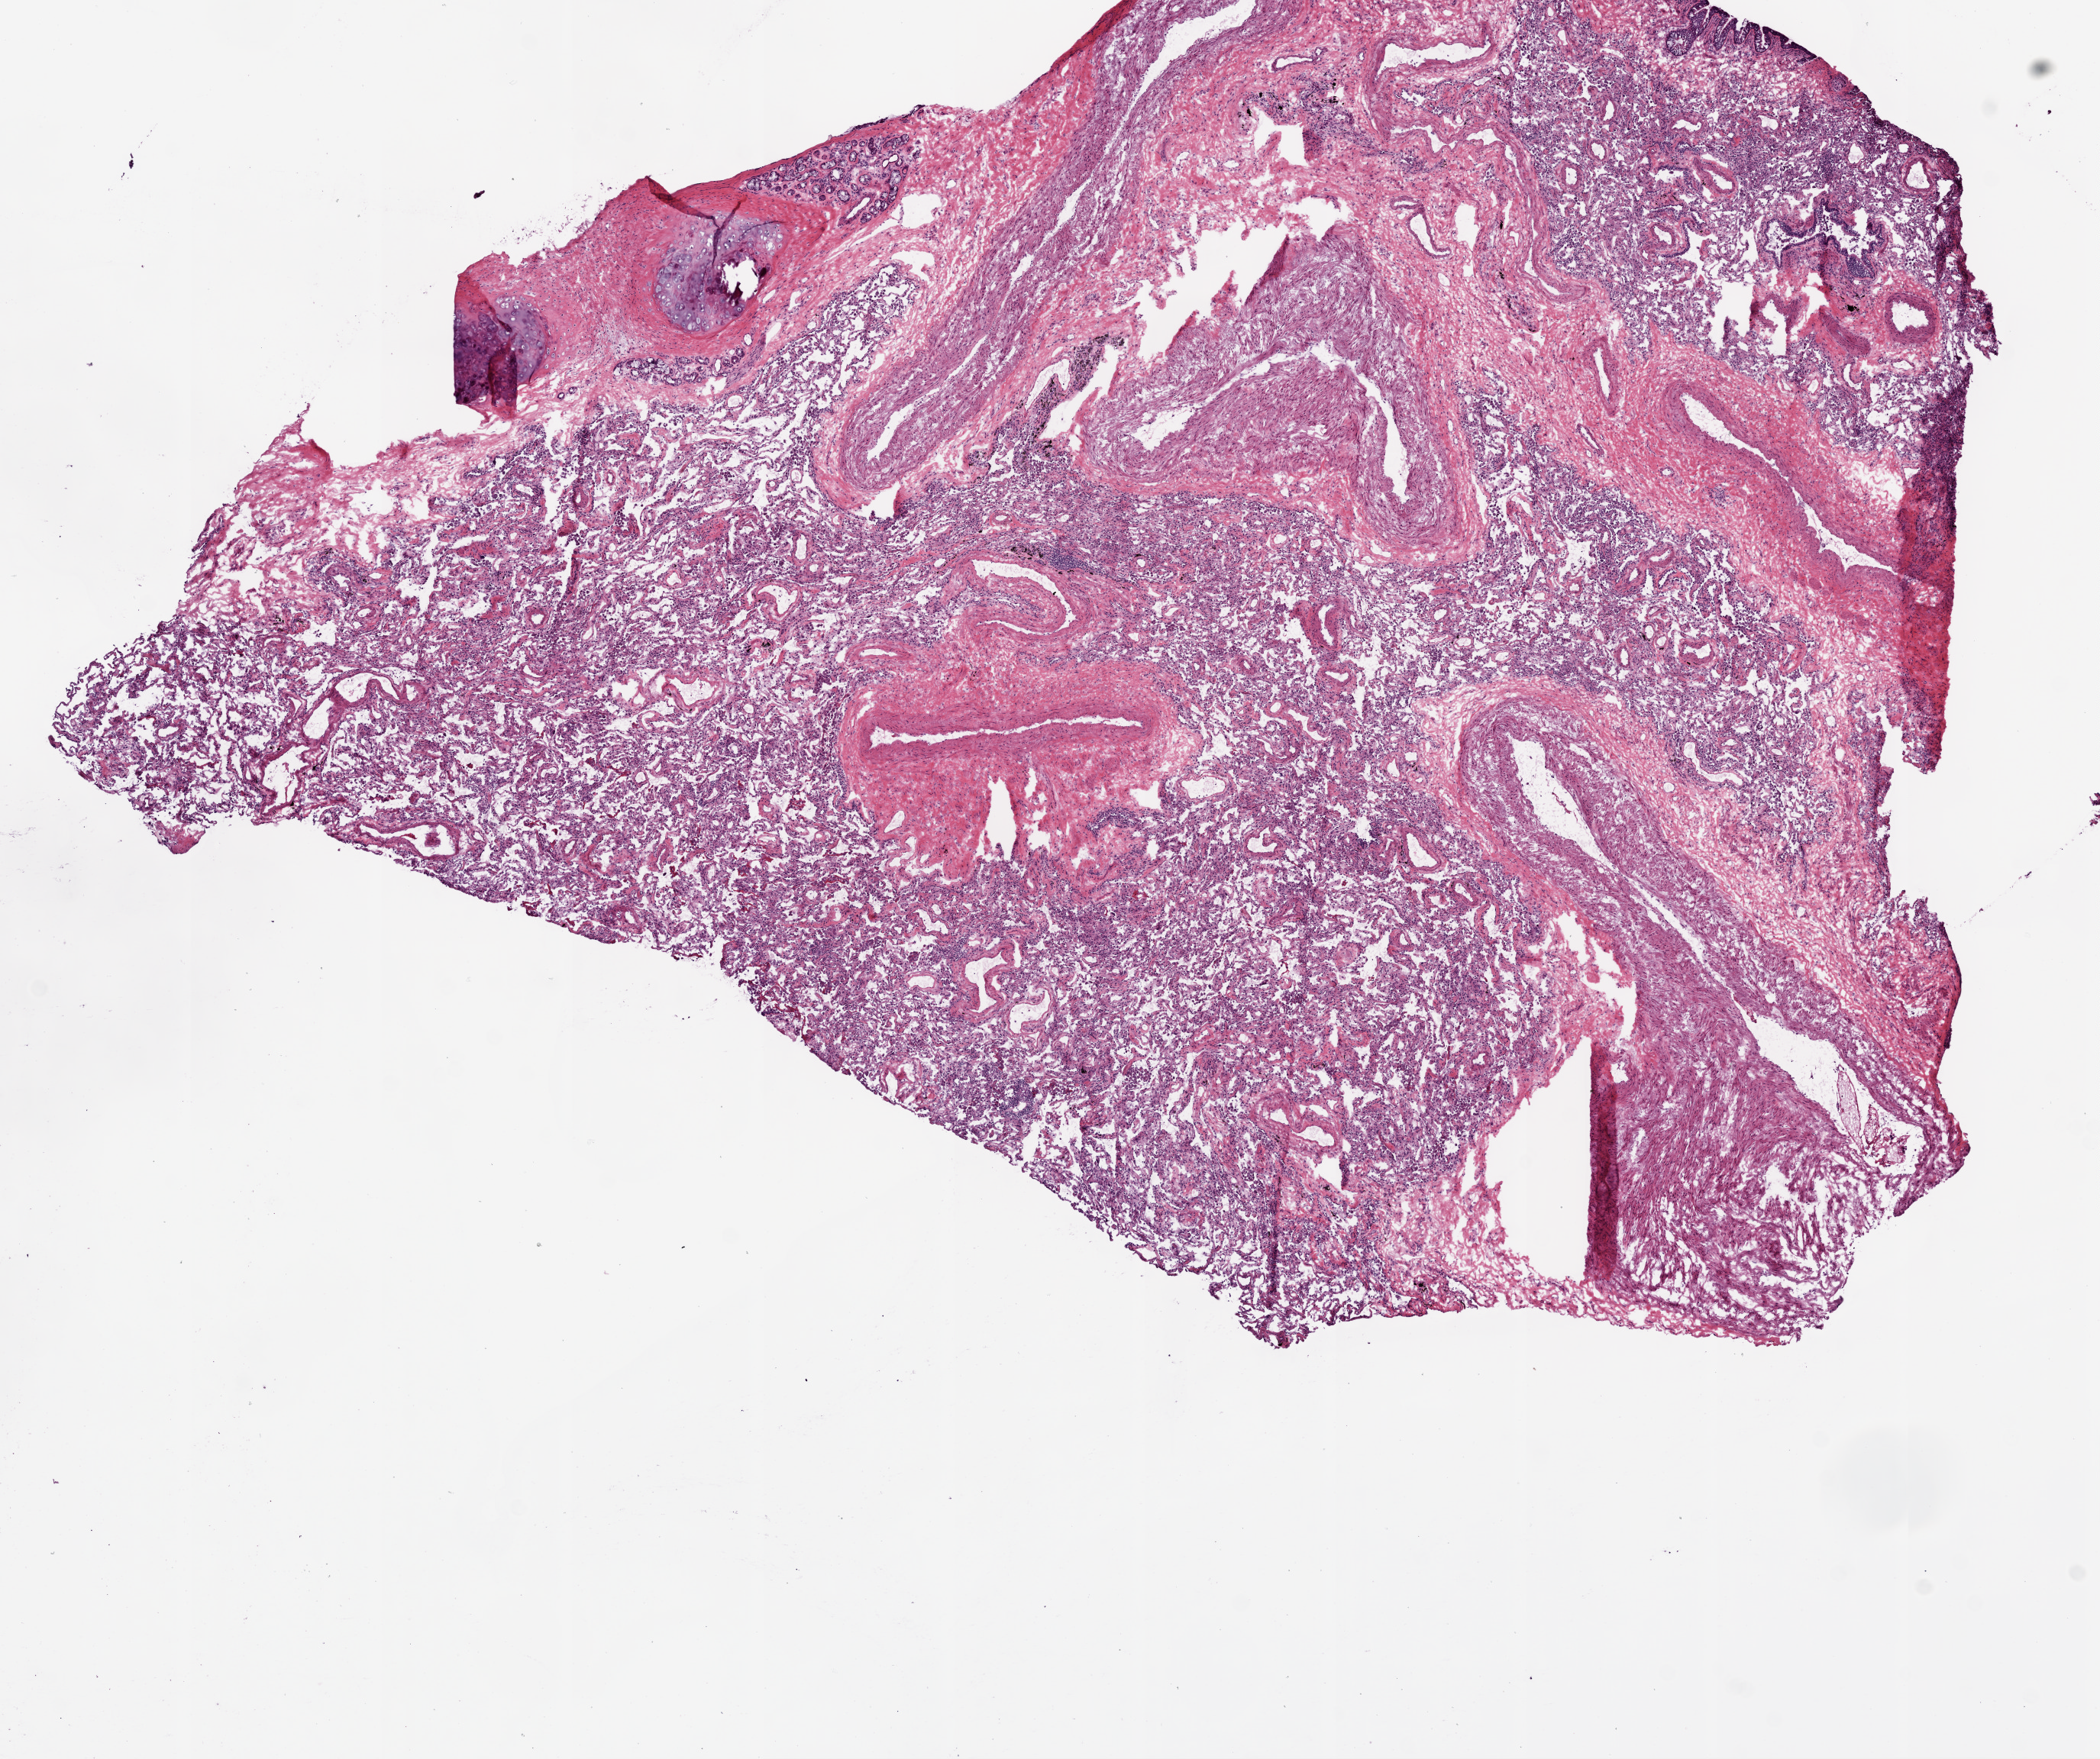
Whole-slide histology image, H&E-stained, shown as a low-resolution overview of the whole scanned area (about 11.0 x 9.2 mm, acquisition: 20x scan); frozen section from the bottom of the tissue portion; sample: solid tissue normal (non-tumour tissue), lung. Female, age 72 years at initial diagnosis.
This section: solid tissue normal (non-tumour) sample from the same patient. Patient diagnosis: Adenocarcinoma, NOS (upper lobe, lung).